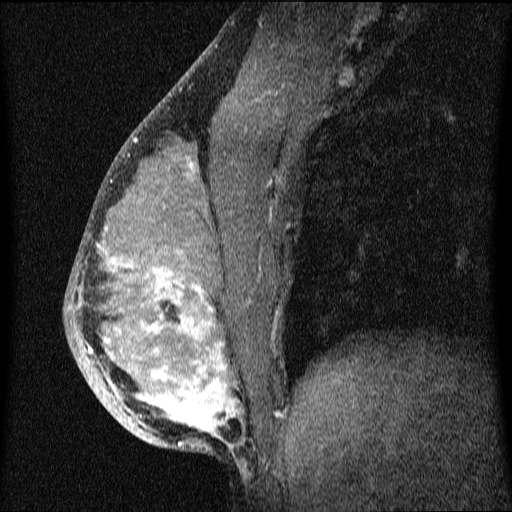
Breast MRI (dynamic contrast-enhanced), one sagittal slice. Position 31 of 64 along the scan axis. Dynamic contrast-enhanced series, image 2 of 4 at this slice position (ordered by acquisition). 1.5 T. TE 4.2 ms, TR 9.1 ms. 2 mm slice thickness. 512 × 512 image matrix. Female patient, age 33 years.
Structures marked on this image (semi-automatically segmented with operator editing):
- analysis volume of interest (the breast-tissue region the enhancement analysis was run in; not a lesion): bounding box [x1, y1, x2, y2] px = [65, 151, 336, 458]
- tumour enhancement mask (voxels above the 70 % enhancement threshold inside the analysis volume of interest): [89, 163, 242, 449]